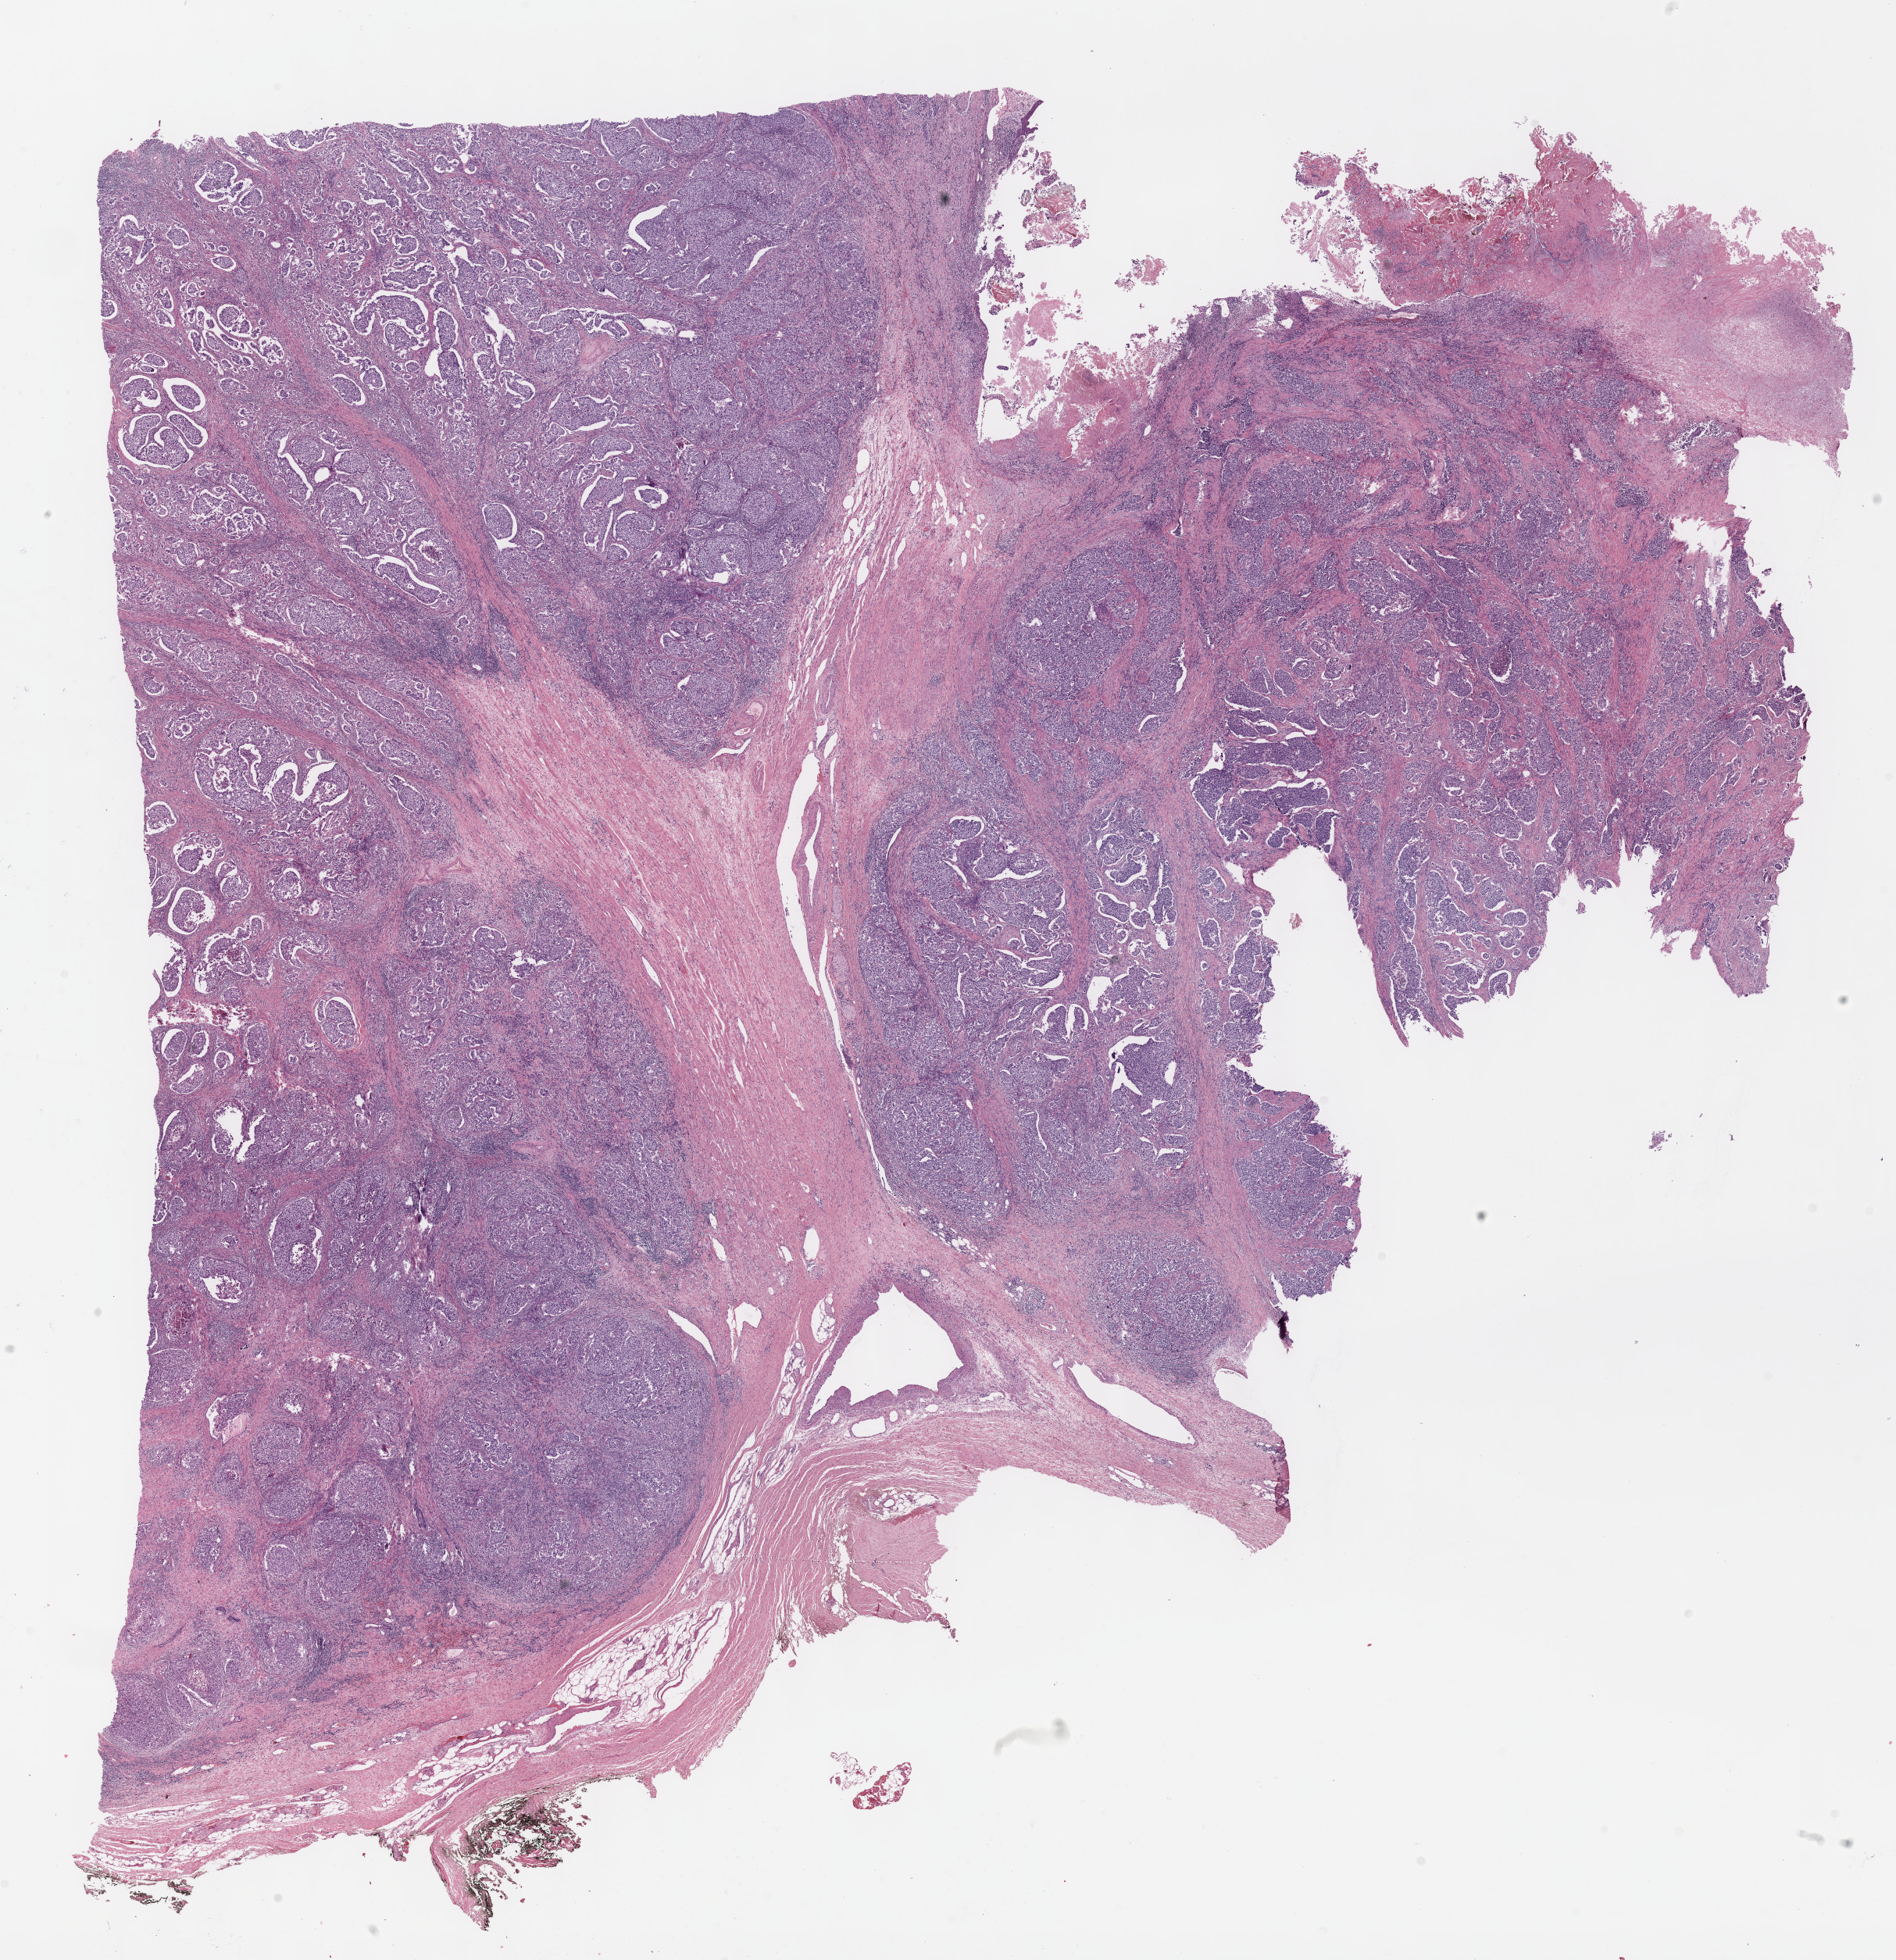
Whole-slide histology image, Hematoxylin and eosin (H&E) stained — whole scanned area (about 19.6 x 20.3 mm) shown as a low-resolution overview, FFPE section, bladder, primary tumour sample. Male patient; age at initial diagnosis 72 years.
Diagnosis: Transitional cell carcinoma.